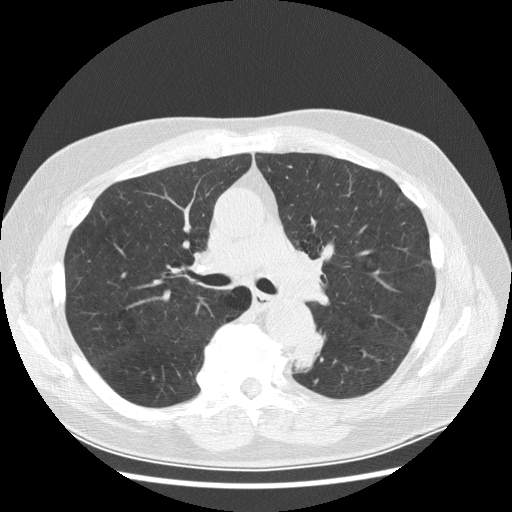
Chest CT (low-dose screening protocol), one axial image, first (baseline) screen, lung window (W 1500 / L -600 HU), 2.5 mm slice thickness, slice 105 of 282 in the series, 512 × 512 image matrix. Male, age 70 years at enrolment. Current smoker at enrolment.
Expert-annotated lung lesion, bounding box <278,329,329,382> (left, top, right, bottom; pixels). Screening reader's record for this exam (one nodule recorded; not confirmed to be the boxed lesion): non-calcified nodule or mass ≥4 mm, left lower lobe, 27 × 16 mm, spiculated (stellate) margins, soft tissue attenuation, pre-existing on the prior screen: yes; interval growth: yes. Official screen result: positive, change unspecified: nodule(s) >= 4 mm or enlarging nodule(s), mass(es), or other non-specific abnormalities suspicious for lung cancer. Later outcome: lung cancer diagnosed 97 days after this screen — papillary adenocarcinoma, NOS, left lower lobe, moderately differentiated (G2), stage IB (AJCC 6th edition), 35 mm at pathology.